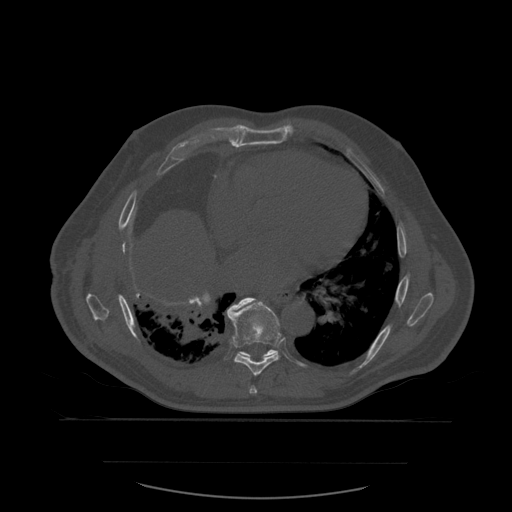
CT including the spine, one axial slice. Position 357 of 590 along the scan axis. Bone window (W 1800 / L 400 HU). 1.25 mm slice thickness. 512 × 512 image matrix, field of view 479 × 479 mm. Patient age 71 years. From the clinical record (not read from this slice): primary cancer: lung; vertebrae with lytic lesions (as recorded): T1, T2, L5, S1.
Annotated regions visible in this slice (semi-automatically segmented with operator editing):
- T7 vertebra: bounding box [x1, y1, x2, y2] px = [250, 386, 258, 394]
- T8 vertebra: [227, 298, 282, 377]
- T9 vertebra: [239, 350, 276, 358]